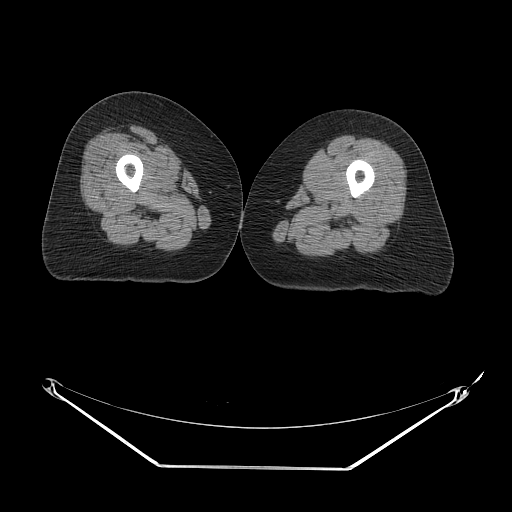
CT of an extremity soft-tissue mass (from a PET/CT study), one axial slice; position 12 of 267 along the scan axis; 140 kVp; soft-tissue window (W 400 / L 40 HU); 3.75 mm slice thickness; 512 × 512 image matrix, field of view 500 × 500 mm. Female patient. From the clinical record (not read from this slice): histological type: malignant solitary fibrous tumor; grade: intermediate; site of the primary tumour: right thigh.
Outlined on this slice (expert contour drawn on MRI and transferred to this co-registered scan by the dataset authors):
- gross tumour volume including surrounding oedema: bounding box [x1, y1, x2, y2] px = [133, 132, 181, 163]